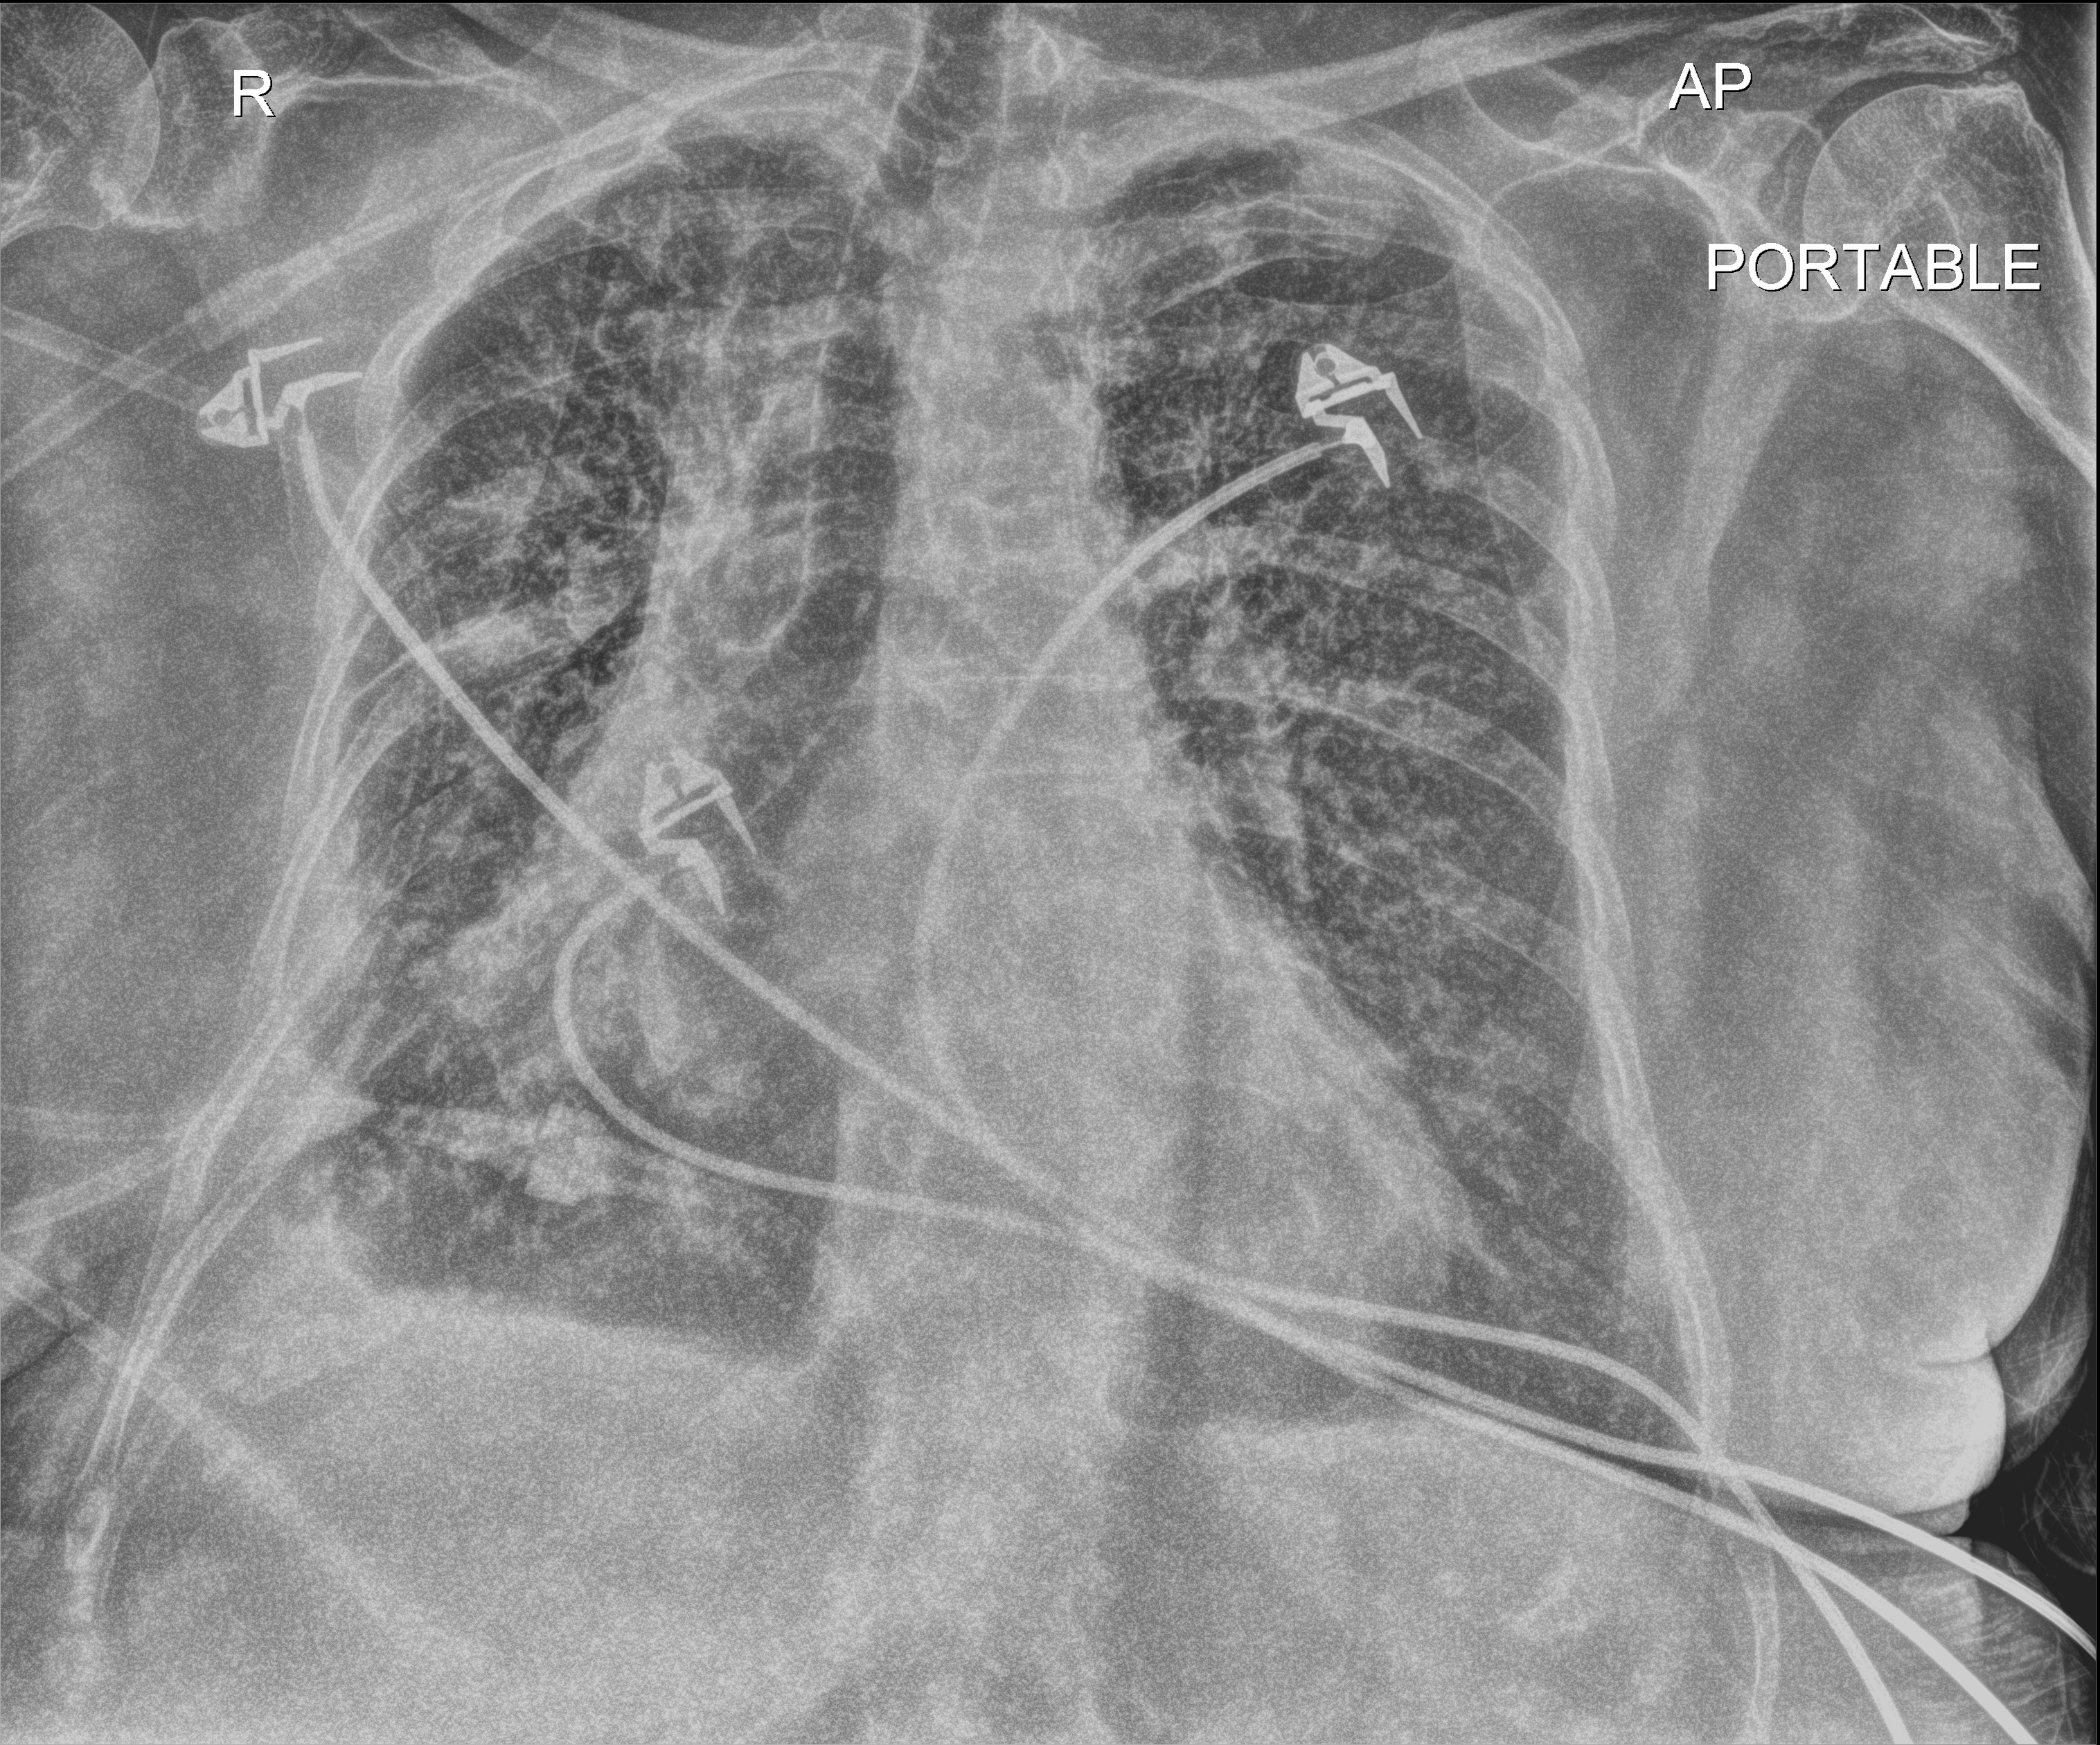
Chest radiograph; anteroposterior (AP) projection. Patient hospitalised with COVID-19; female, aged 75–90 years.
From the hospital-stay record, not from the radiograph (when in the stay this image was taken is not recorded): mechanically ventilated during this hospital stay: no; admitted to intensive care during this hospital stay: no.